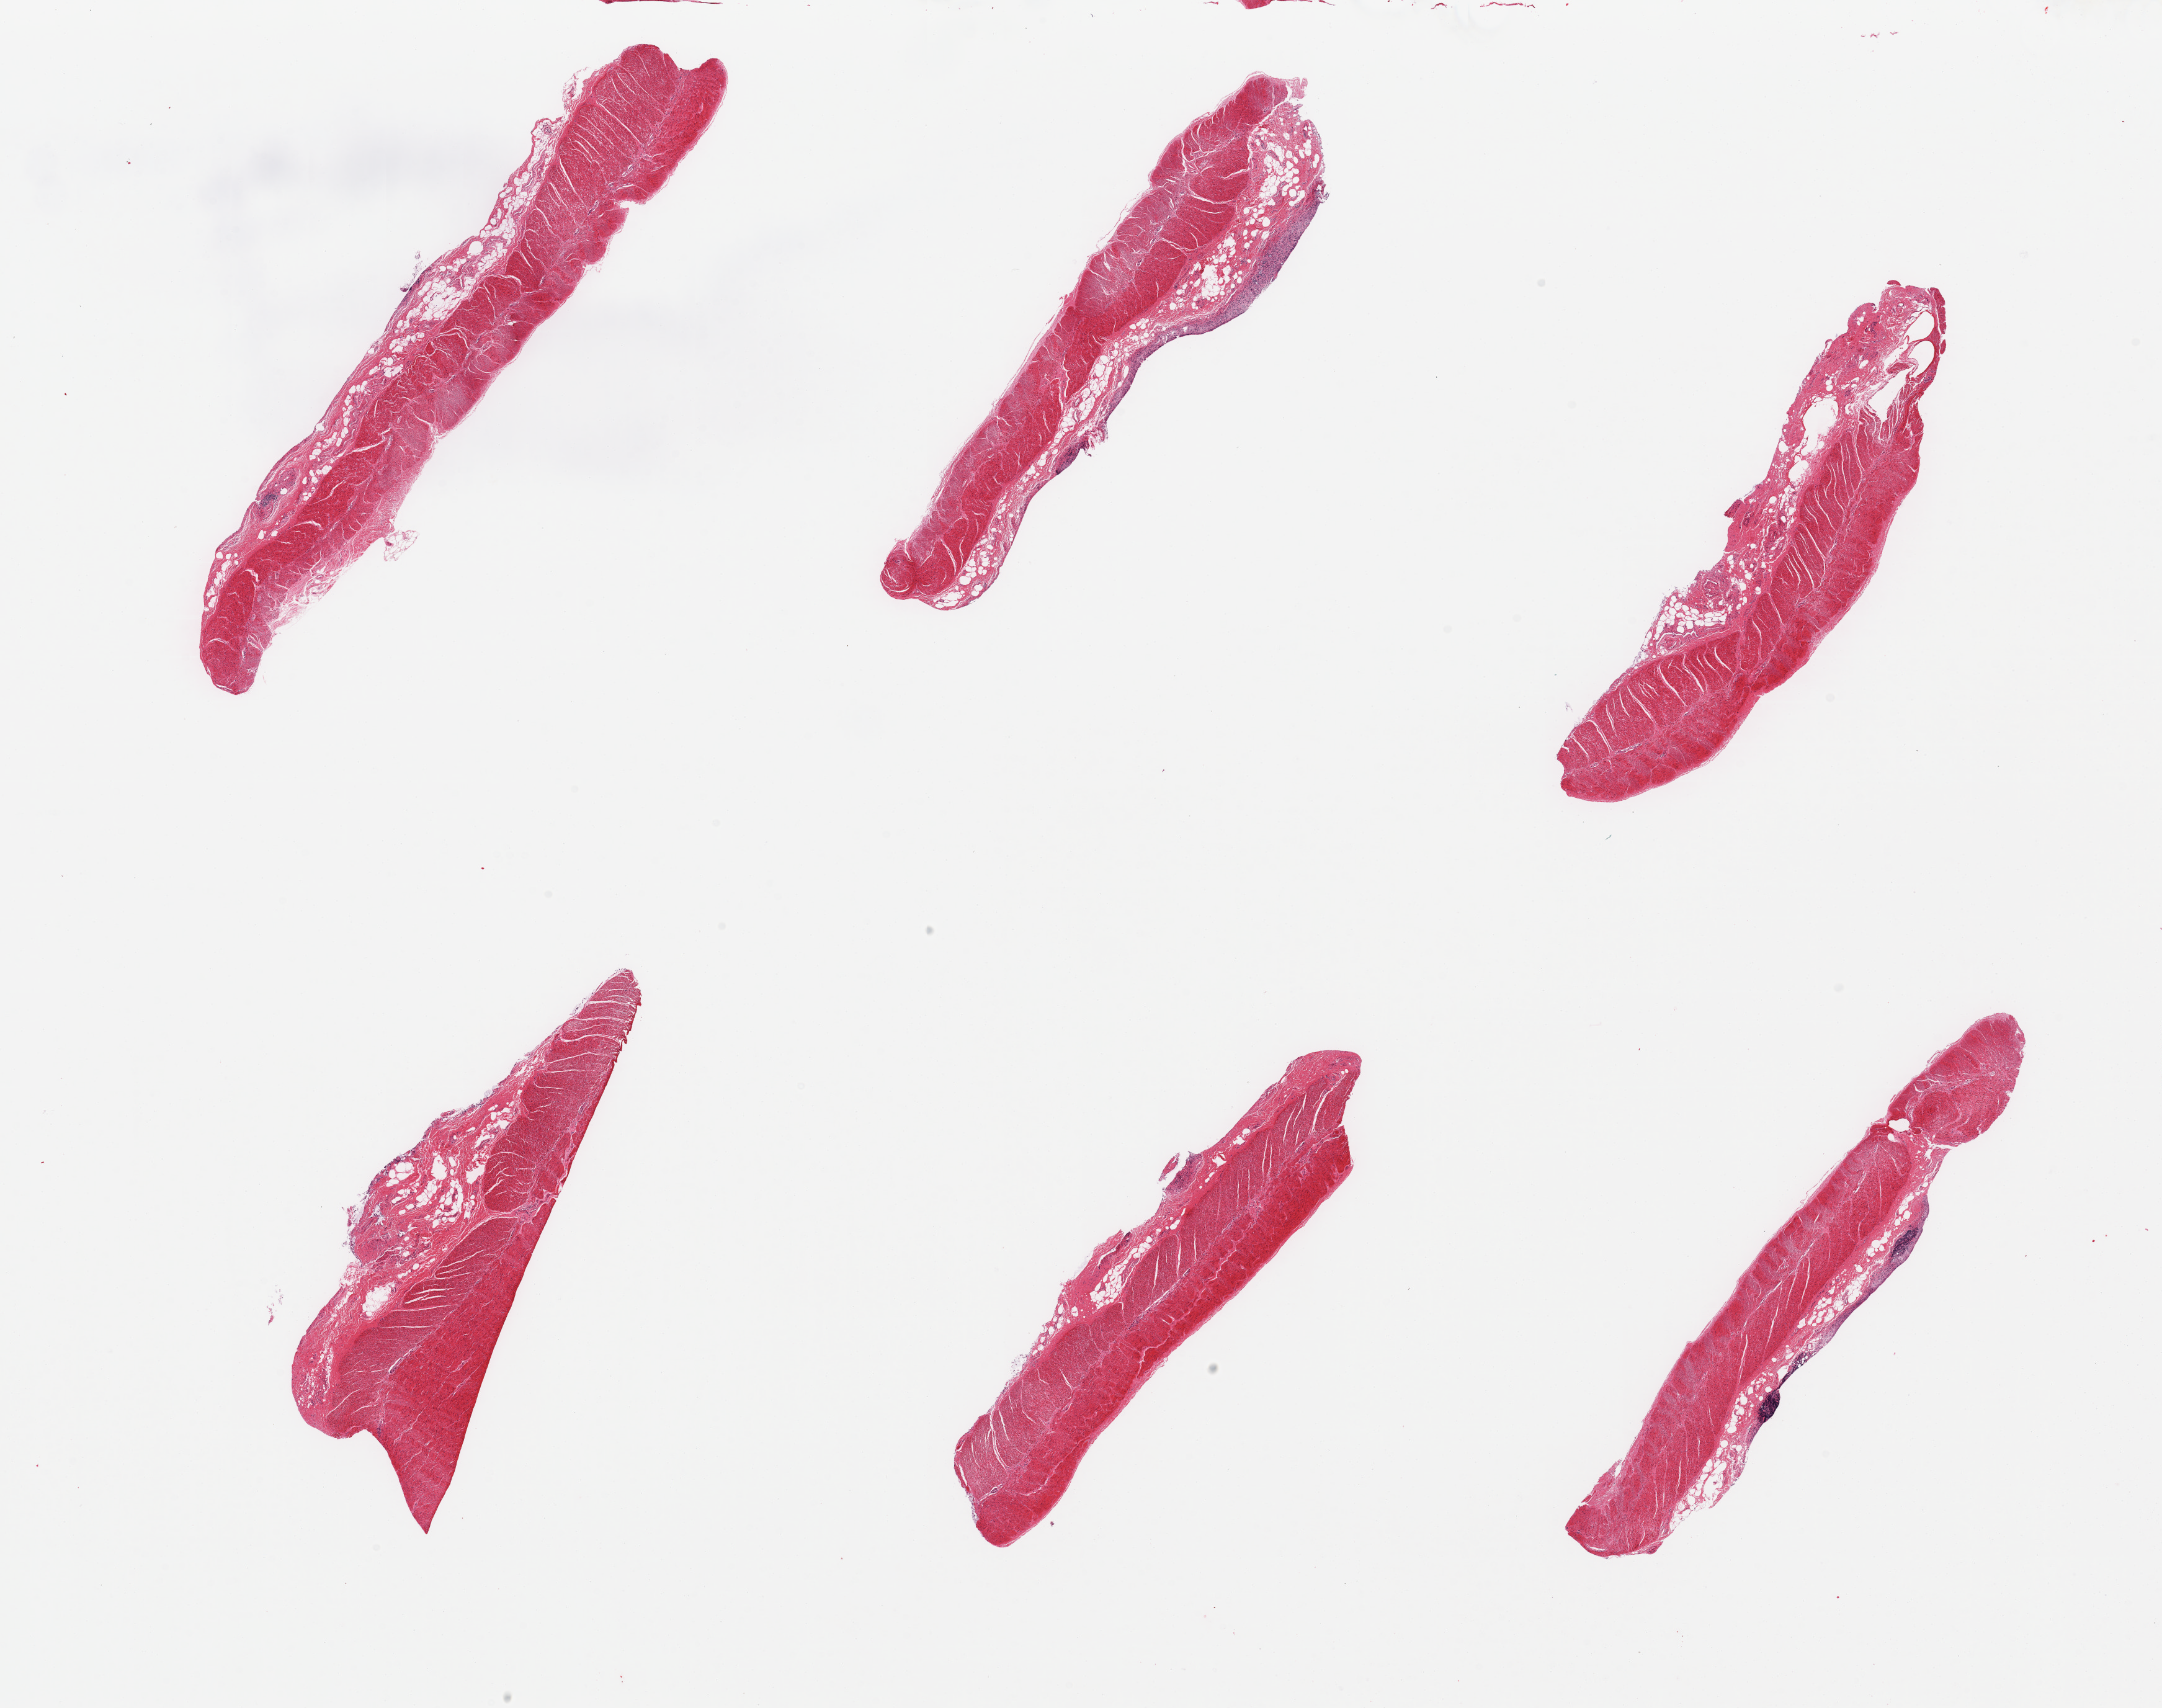
Hematoxylin and eosin (H&E) whole-slide image, whole scanned area (about 27.6 x 21.8 mm, slide scanned at 20x) shown as a low-resolution overview. PAXgene-fixed paraffin-embedded (PFPE) section. Target tissue: sigmoid colon. Tissue donor sample.
Review note (as recorded): 6 pieces, confirmed target muscularis.